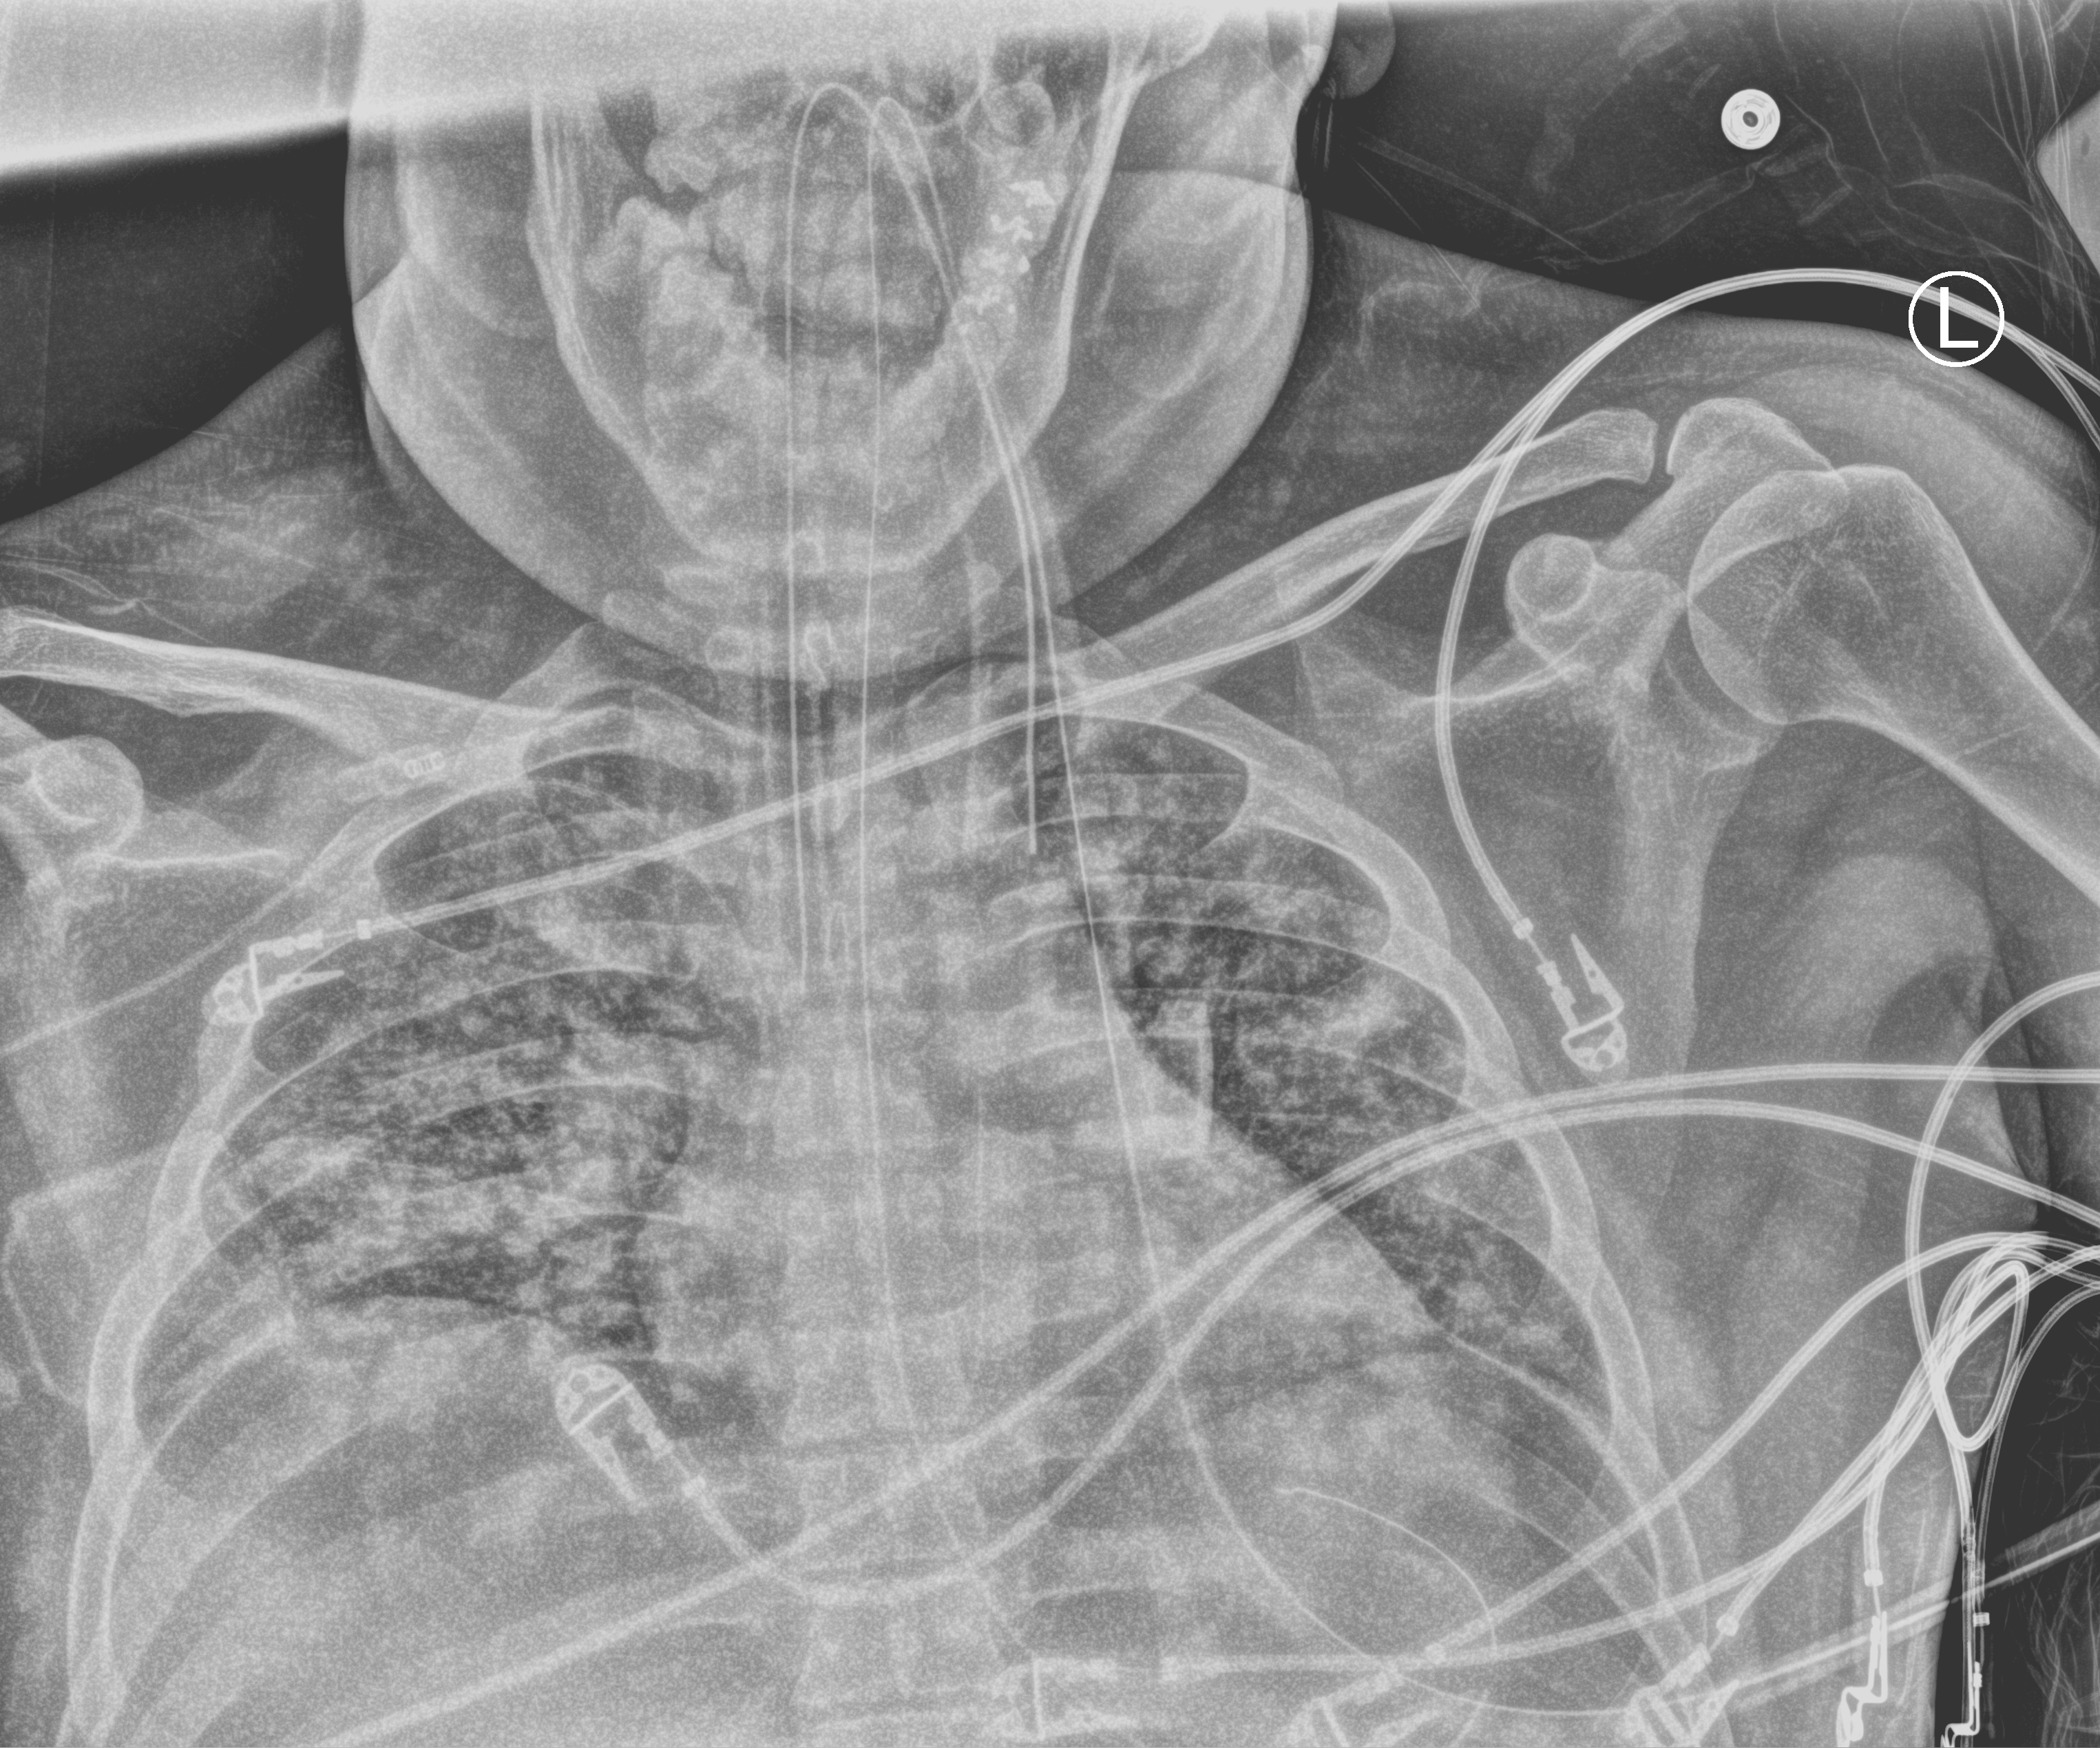
Bedside chest radiograph (computed radiography); anteroposterior (AP) projection. Male patient hospitalised with COVID-19, age 18–59 years.
From the hospital-stay record, not from the radiograph (when in the stay this image was taken is not recorded): mechanically ventilated during this hospital stay: yes; length of hospital stay: 44 days.